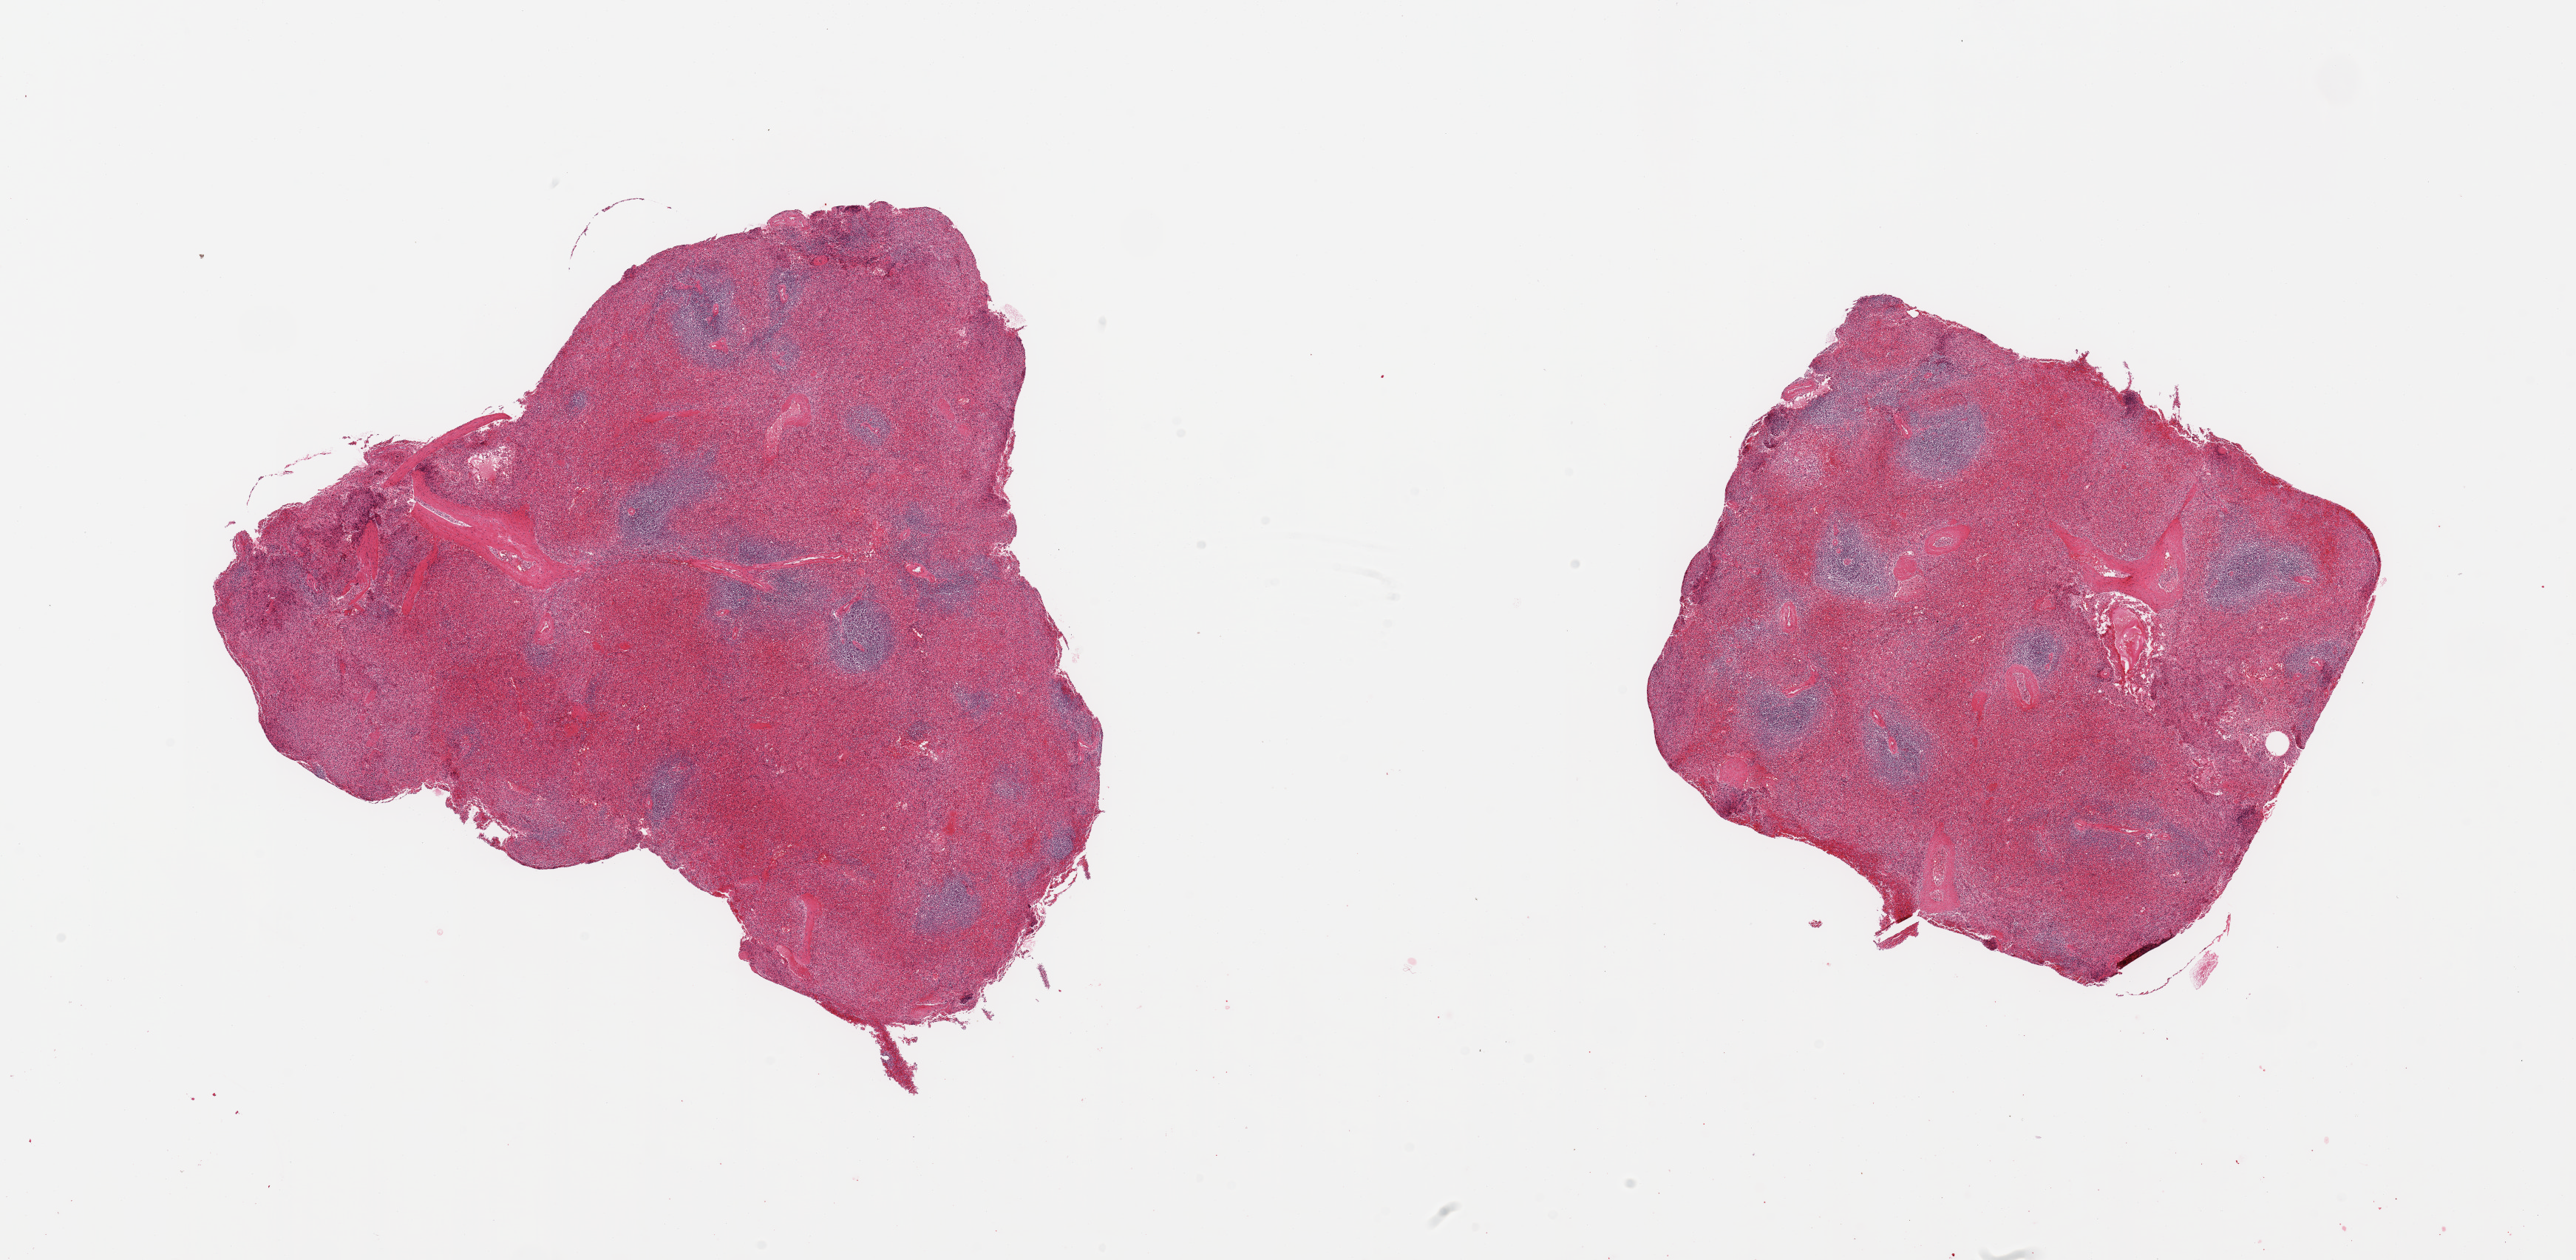
Haematoxylin and eosin whole-slide image, low-resolution overview of the scanned area, about 27.6 x 13.5 mm (acquisition: 20x scan); PAXgene-fixed, paraffin-embedded tissue; sampled site (target tissue): spleen; donor tissue sample. Donor: male.
- pathologist's review note for this sample: 2 pieces; moderate vascular congestion in red pulp; well defined lymphoid tissue (white pulp)